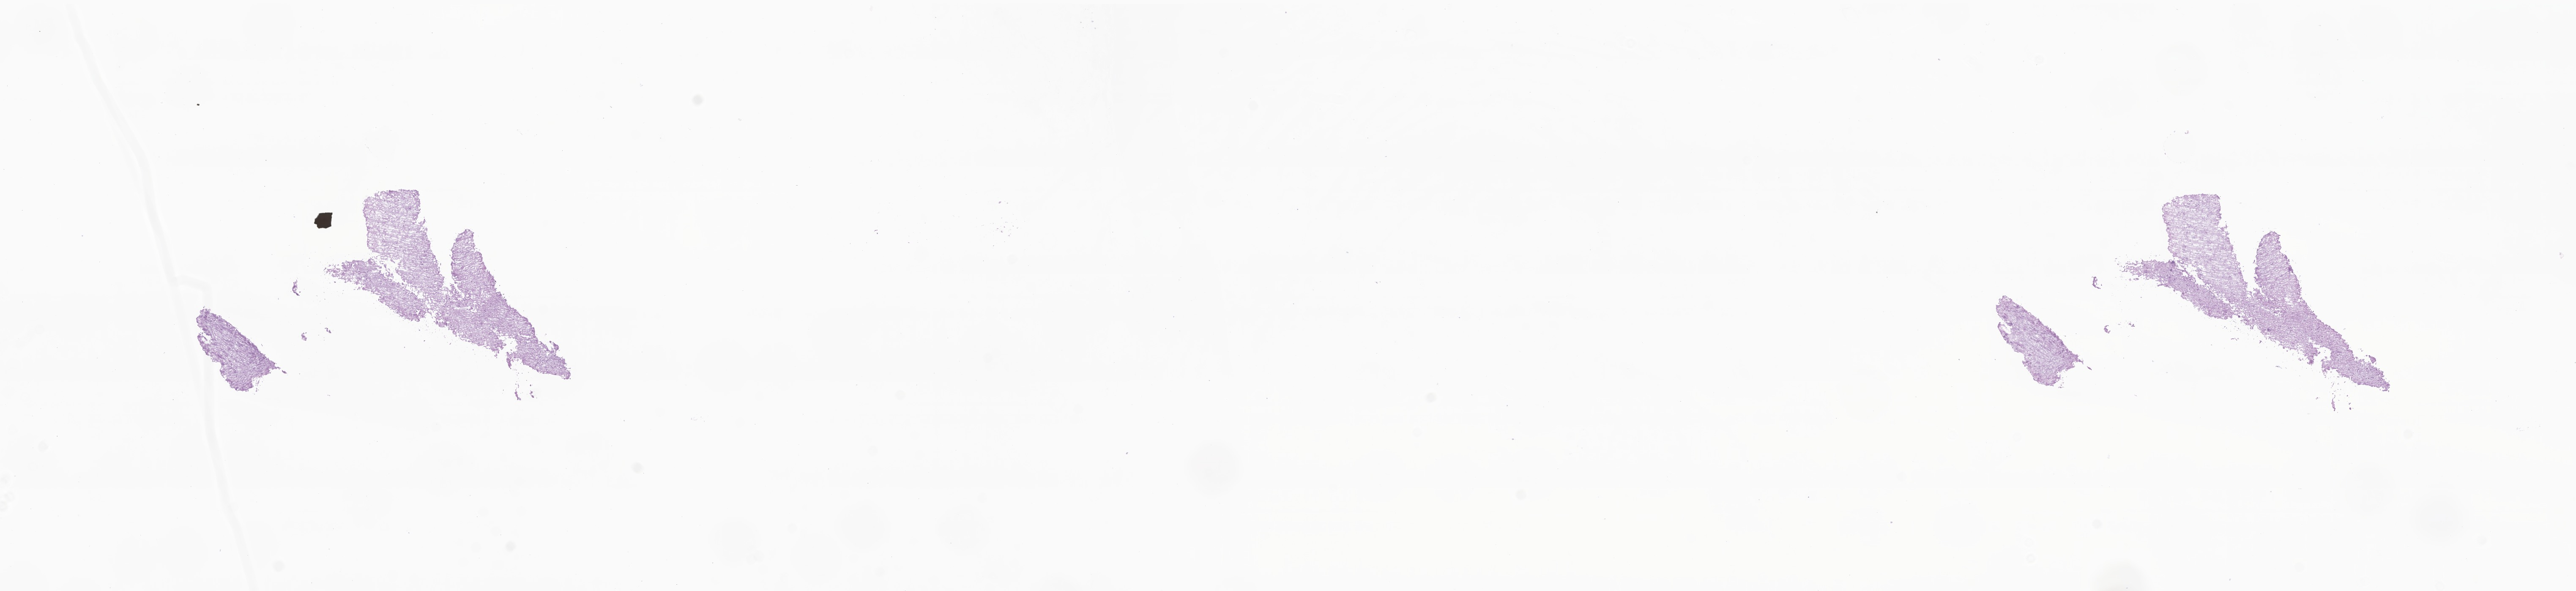
Digitized H&E-stained section of tumor tissue from the temporal lobe, shown as a low-resolution overview of the whole scanned area (about 25.7 x 5.9 mm), cryosection (OCT / tissue freezing medium). Female patient, age 143 months (11 years 11 months).
• diagnosis (ICD-O-3 morphology term): Oligoastrocytoma, NOS